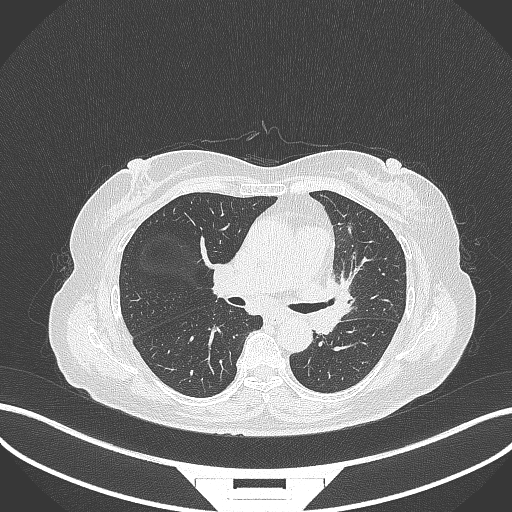
Chest CT, one axial slice. Position 190 of 382 along the scan axis. 120 kVp. Lung window (W 1500 / L -600 HU). 1 mm slice thickness. 512 × 512 image matrix, field of view 400 × 400 mm. Female patient, age 64 years. From the clinical record (not read from this slice): clinical TNM (as recorded): T2a N2 M0.
Outlined on this slice (bounding box drawn by a radiologist):
- lung tumour (recorded histology: adenocarcinoma): bounding box [x1, y1, x2, y2] px = [319, 273, 362, 337]